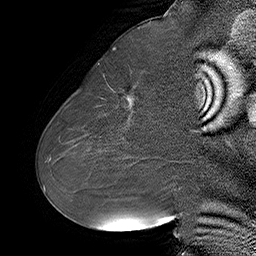
Breast MRI (dynamic contrast-enhanced), one sagittal slice; position 30 of 55 along the scan axis; dynamic contrast-enhanced series, time point 2 of 6 at this slice position (early post-contrast); 1.5 T; TE 4.5 ms, TR 32.4 ms; 256 × 256 image matrix, field of view 180 × 180 mm. Female patient. Case-level facts recorded for this patient, not image findings: setting: breast cancer imaged before/during neoadjuvant chemotherapy; receptor status: HER2-positive.
Annotated regions visible in this slice (semi-automatically segmented with operator editing):
- analysis volume of interest (the breast-tissue region the enhancement analysis was run in; not a lesion): bounding box (x1, y1, x2, y2) in pixels: (80, 64, 163, 134)
- tumour enhancement mask (voxels above the 100 % enhancement threshold inside the analysis volume of interest): (127, 96, 132, 108)